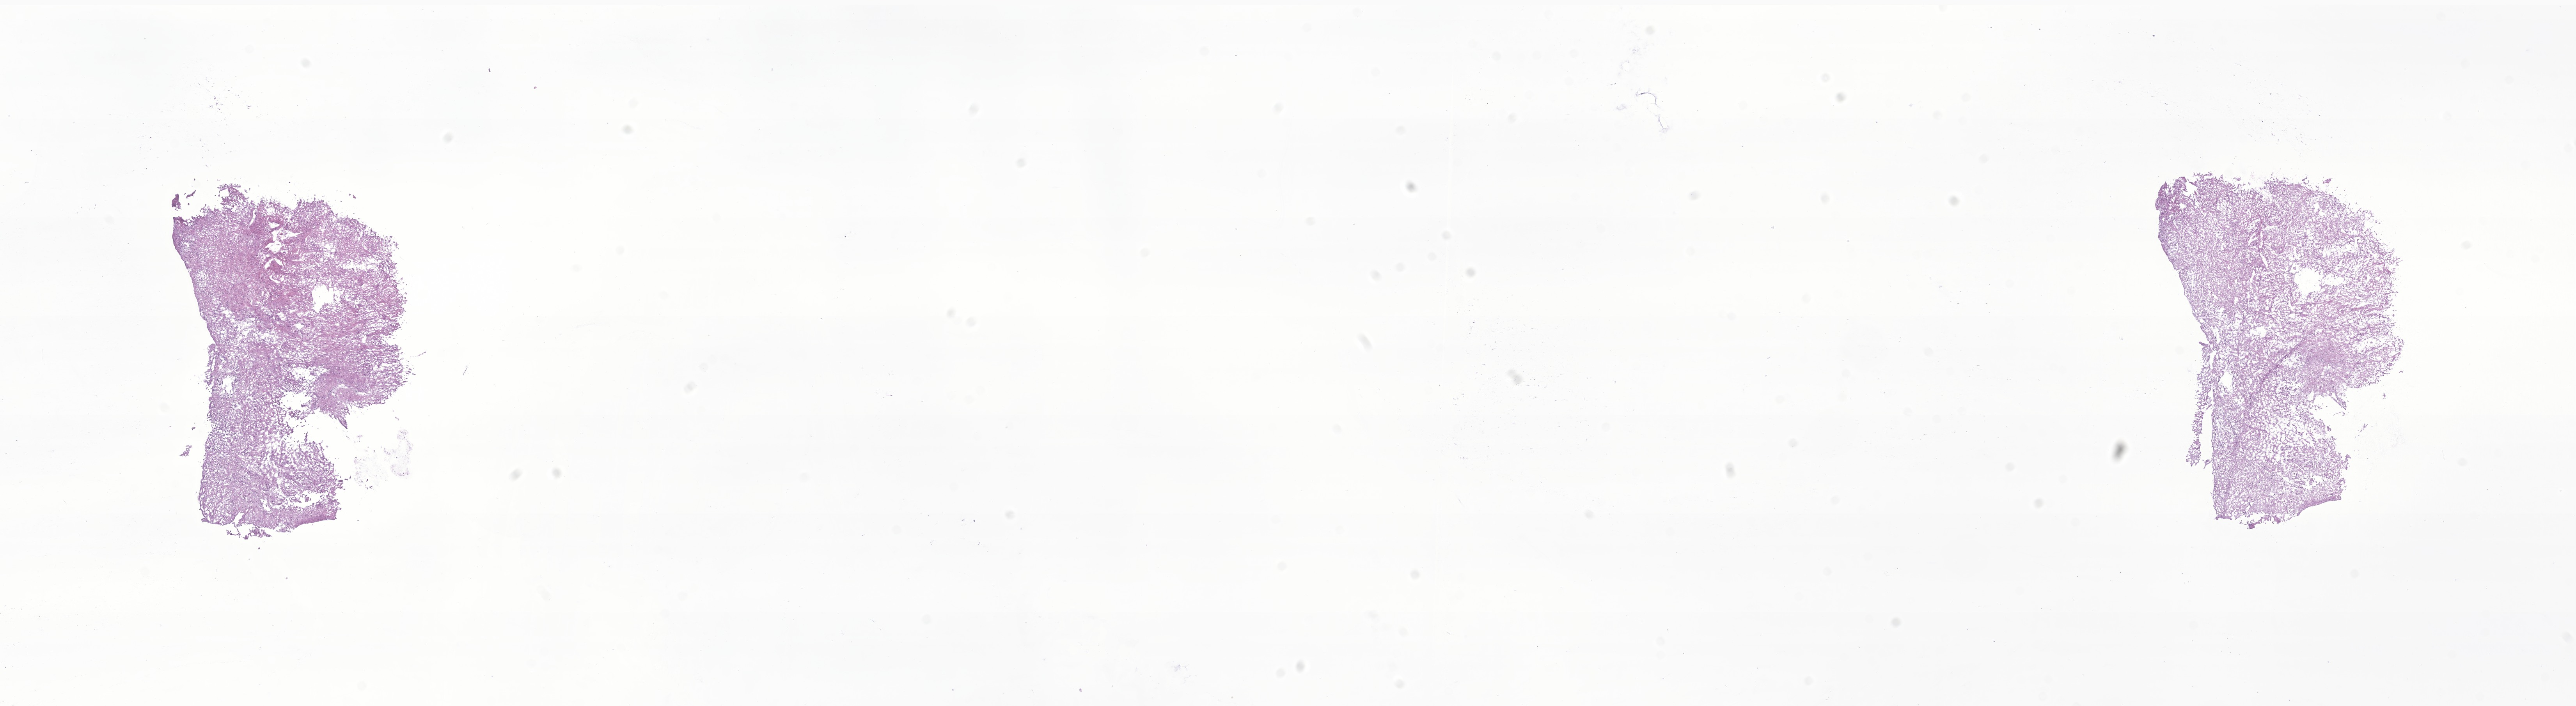
Whole-slide image, haematoxylin and eosin stain of tumor tissue from the cerebellum, a low-resolution overview of the entire scanned area, about 27.8 x 7.6 mm; frozen section. Patient male; age 62 months (5 years 2 months).
- diagnosis: Pilocytic astrocytoma